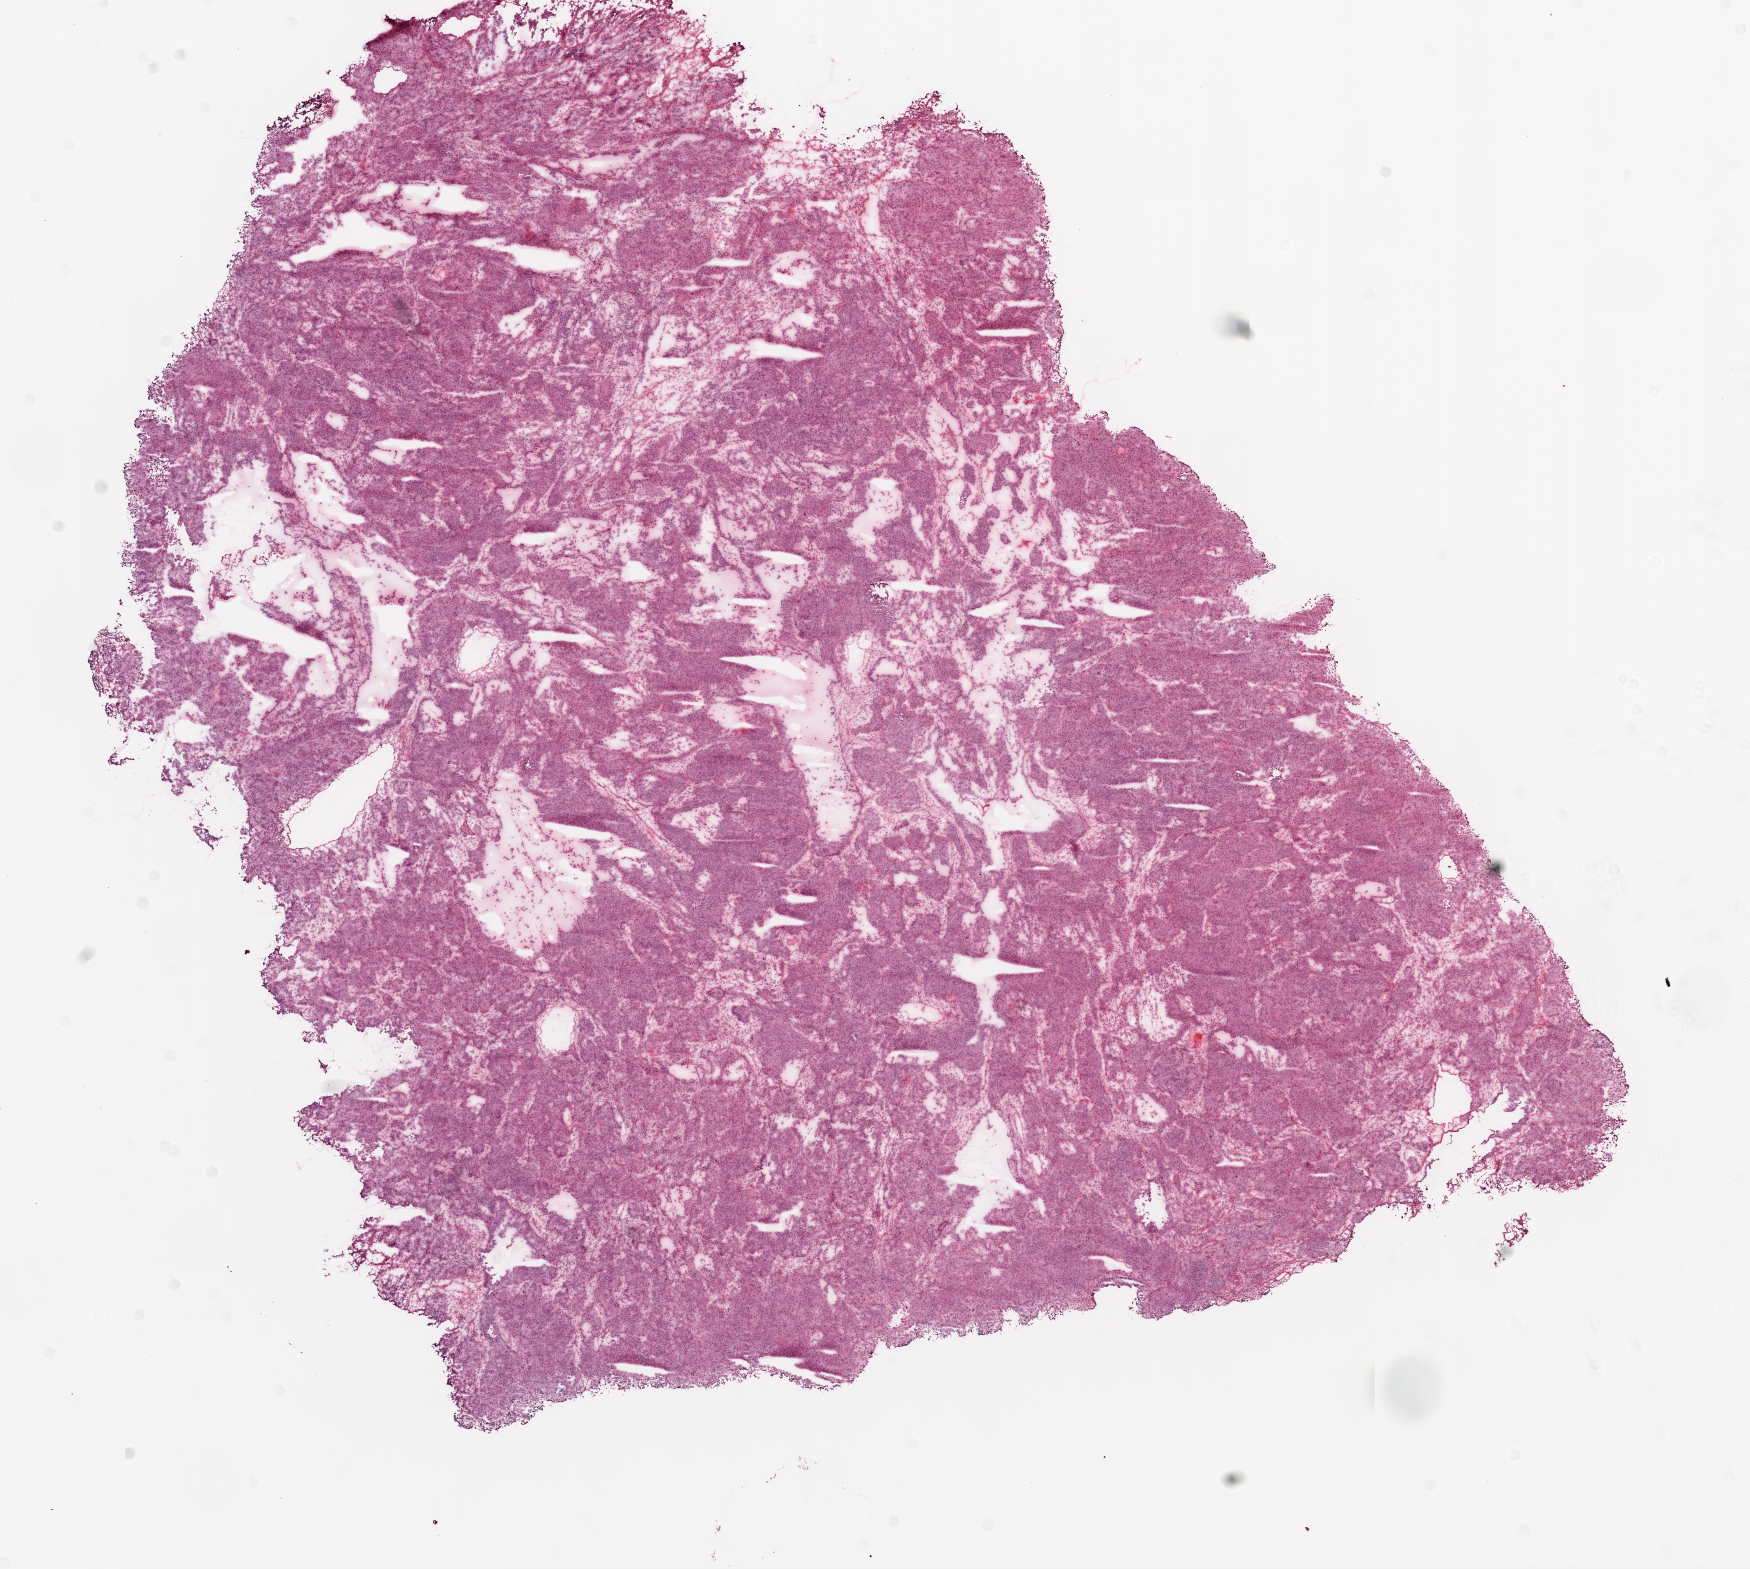
Digitized H&E-stained tissue section (whole slide), shown as a low-resolution overview of the whole scanned area (about 14.0 x 12.6 mm), frozen section, sample: primary tumour, ovary. Female patient; age at initial diagnosis 60 years. Pathologist review of this section (percent, as recorded): tumour cells 95%, tumour nuclei 98%.
Diagnosis: Serous cystadenocarcinoma, NOS.